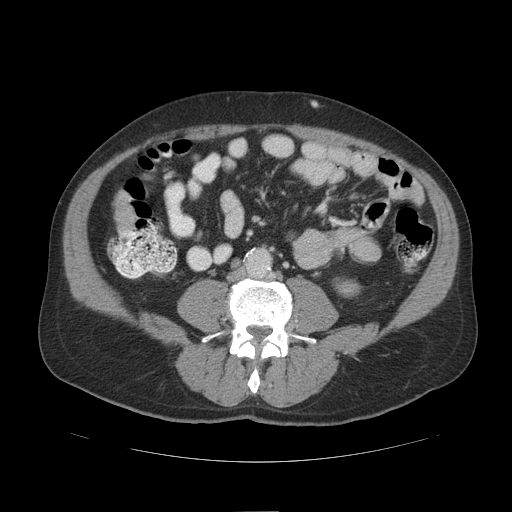
Contrast-enhanced abdominal CT (liver protocol), one axial slice. Position 20 of 109 along the scan axis. Reconstruction kernel STANDARD. Soft-tissue window (W 400 / L 40 HU). 512 × 512 image matrix. From the clinical record (not read from this slice): diagnosis: hepatocellular carcinoma (patient treated with transarterial chemoembolisation; whether this scan precedes or follows treatment is not stated here); TNM stage (as recorded): Stage-IIIB; Child-Pugh class: A; tumour differentiation: poorly differentiated; tumour nodularity: multinodular.
Structures marked on this image (semi-automatically segmented with operator editing):
- liver parenchyma outside the tumour (the mass and vessels are separate outlines, so this box may not span the whole liver): box from (x=116, y=194) to (x=134, y=228) px